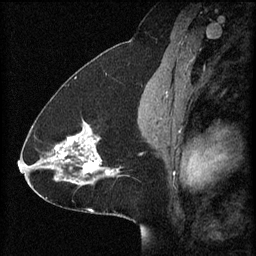
Breast MRI (dynamic contrast-enhanced), one sagittal slice. Position 33 of 60 along the scan axis. 3 images stored at this slice position (order not interpretable as contrast timing). 1.5 T. TE 4.2 ms, TR 8.2 ms. 2 mm slice thickness. 256 × 256 image matrix. Patient: female, 41 years.
Outlined on this slice (semi-automatic segmentation, software-assisted and operator-edited):
- analysis volume of interest (the breast-tissue region the enhancement analysis was run in; not a lesion): bounding box [x1, y1, x2, y2] px = [58, 118, 128, 181]
- tumour enhancement mask (voxels above the 70 % enhancement threshold inside the analysis volume of interest): [58, 122, 121, 181]